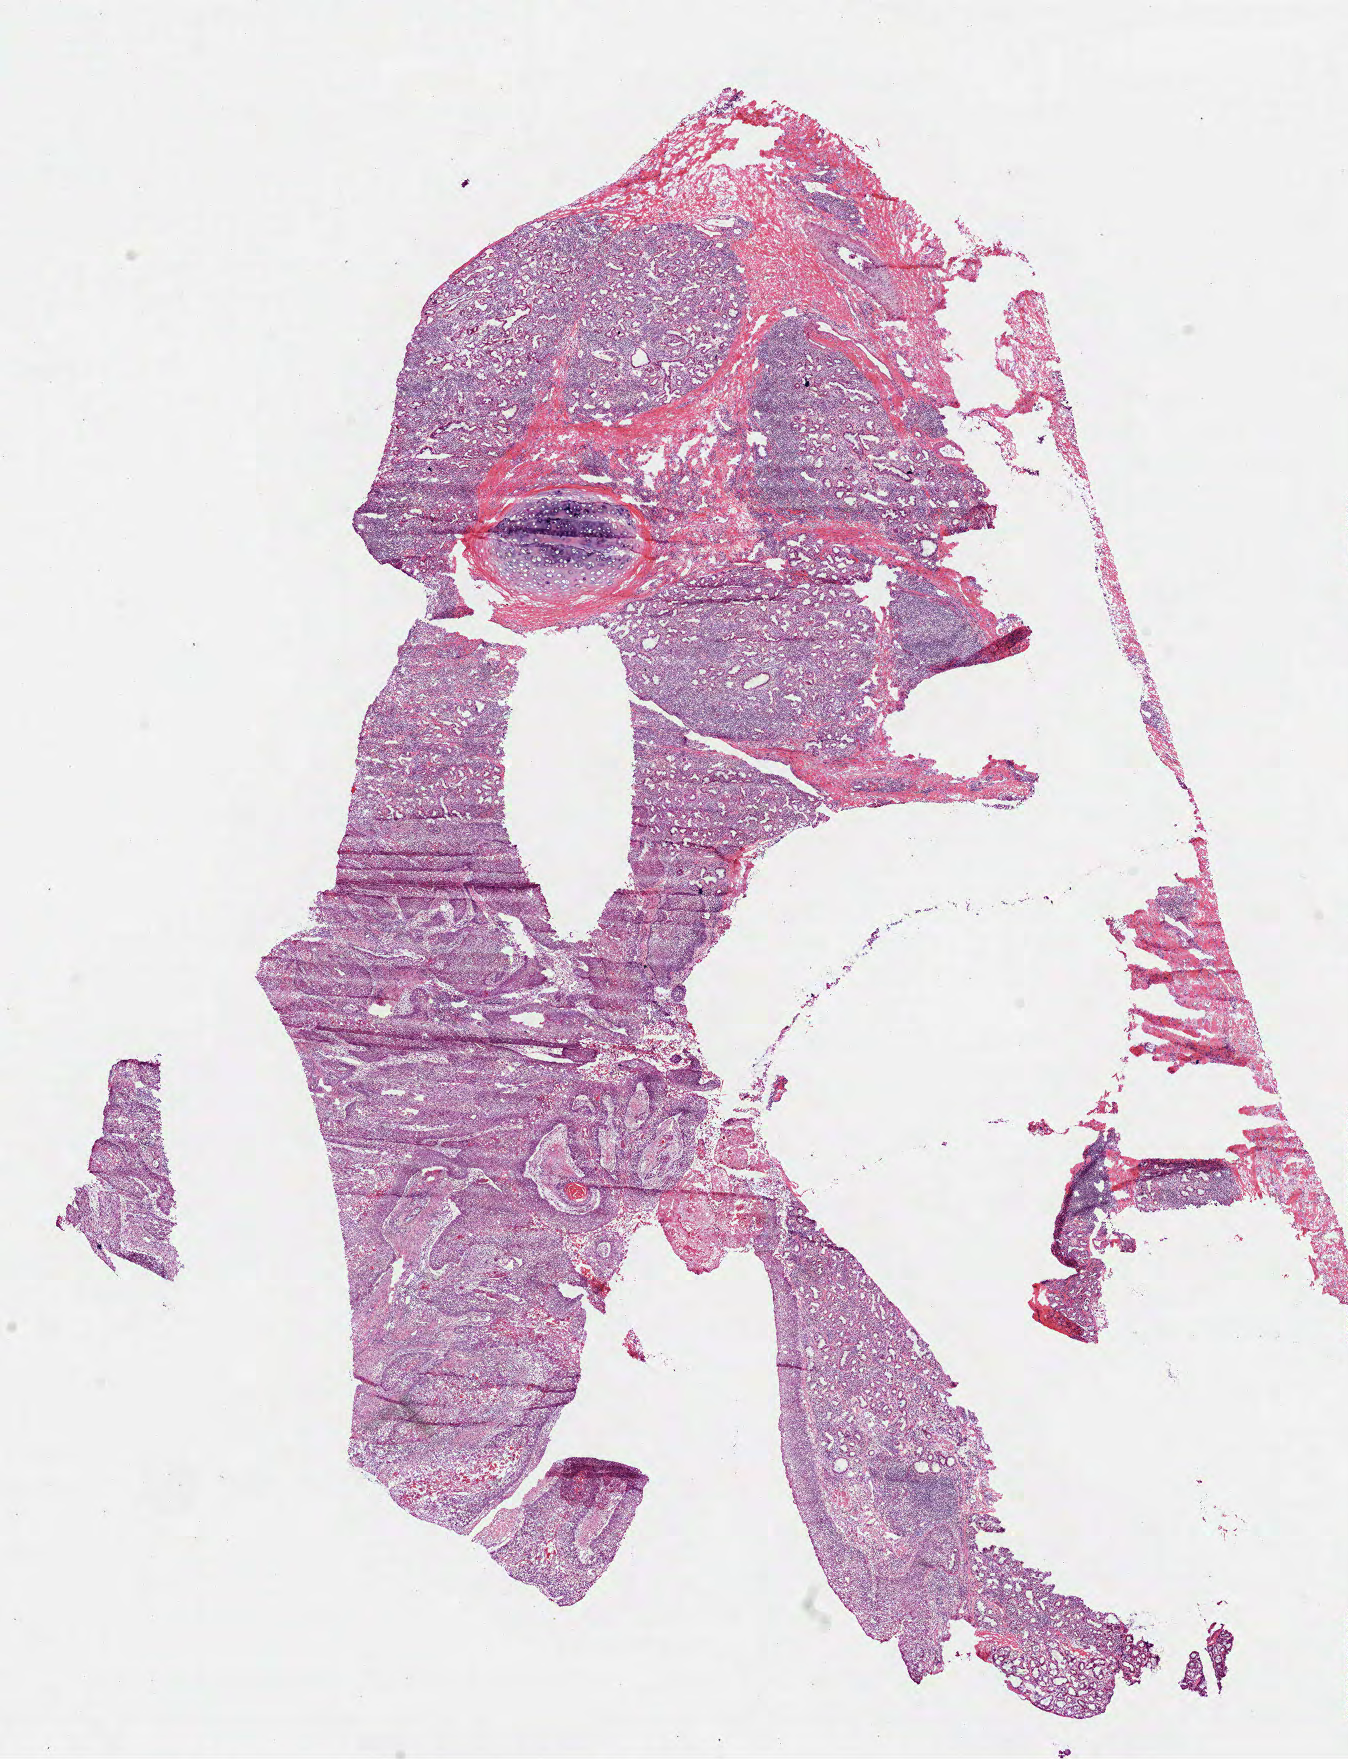
Digitized Hematoxylin and eosin (H&E) stained tissue section (whole slide), low-resolution overview of the scanned area, about 10.9 x 14.2 mm (acquisition: 40x scan), frozen section from the bottom of the tissue portion, sample: primary tumour, lung. Male patient; age at initial diagnosis 49 years. Composition of this section per pathologist review: tumour cells 30%, tumour nuclei 28%, normal cells 55%, stromal cells 13%, necrosis 2%. Infiltration values recorded for this section: lymphocyte infiltration 12%.
* TNM: T3 N0 M0
* AJCC pathologic stage: IIB (7th edition)
* diagnosis: Squamous cell carcinoma, NOS (upper lobe, lung)